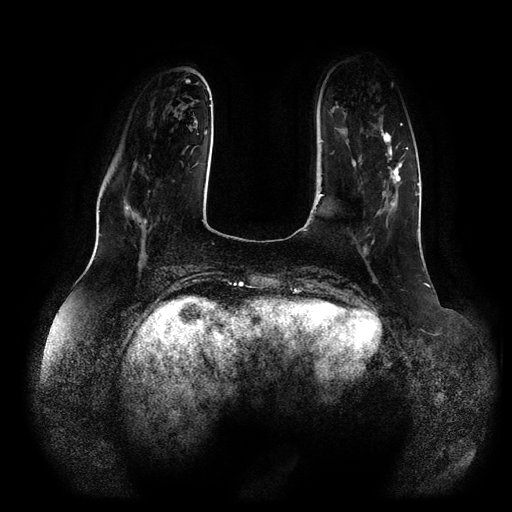
Breast MRI (dynamic contrast-enhanced, multi-phase), one axial slice; dynamic contrast-enhanced series, time point 2 of 5 at this slice position (early post-contrast); 1.5 T; TE 2.5 ms, TR 5.2 ms; 2 mm slice thickness; 512 × 512 image matrix, field of view 400 × 400 mm. Female patient, age 66 years.
Annotated regions visible in this slice (semi-automatic segmentation, software-assisted and operator-edited):
- breast lesion (labelled 'tumour' in the annotation; benign lesions carry a separate 'benign' label): box from (x=381, y=127) to (x=408, y=210) px